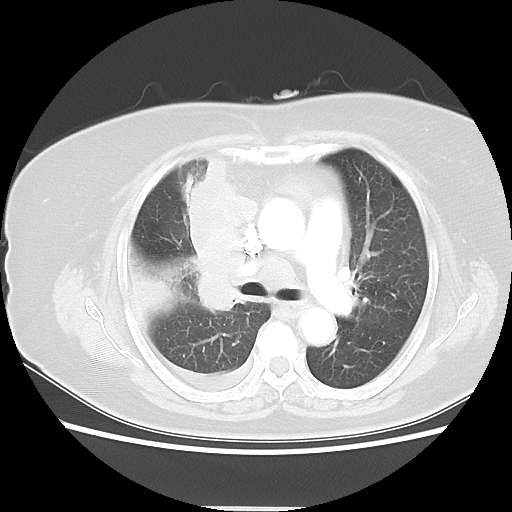
Chest CT, one axial slice. Position 30 of 48 along the scan axis. Reconstruction kernel LUNG. Lung window (W 1500 / L -600 HU). 5 mm slice thickness. 512 × 512 image matrix. Female patient, age 73 years. From the clinical record (not read from this slice): clinical TNM (as recorded): T3 N3 M1b.
Outlined on this slice (rectangle marked by the reading radiologist):
- lung tumour (recorded histology: small cell carcinoma): box from (x=176, y=143) to (x=271, y=326) px